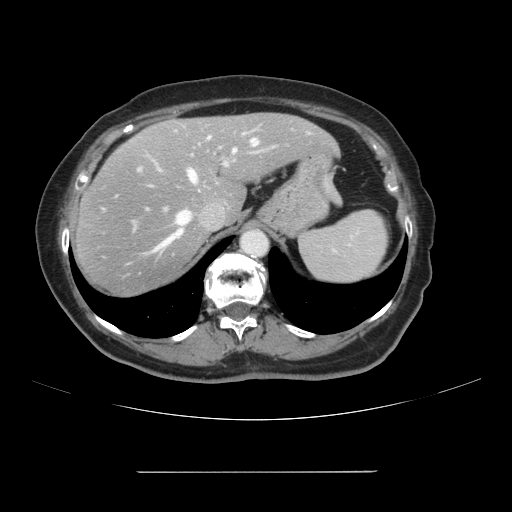
Contrast-enhanced abdominal CT, one axial slice; slice 79 of 111 in the series (ordered by position); 120 kVp; intravenous contrast given; soft-tissue window (W 400 / L 40 HU); 2.5 mm slice thickness; 512 × 512 image matrix, field of view 400 × 400 mm. Female patient, age 74 years. Case-level facts recorded for this patient, not image findings: diagnosis: colorectal cancer liver metastases, imaged before liver resection; multiple liver metastases: yes; largest metastasis: 1.1 cm.
Structures marked on this image (outlined manually by an expert reader):
- hepatic veins: box from (x=128, y=139) to (x=258, y=264) px
- liver: (x=73, y=113)–(x=334, y=296)
- planned liver remnant (the part of the liver to remain after resection): (x=159, y=113)–(x=334, y=220)
- portal vein (with intrahepatic branches): (x=139, y=134)–(x=244, y=171)